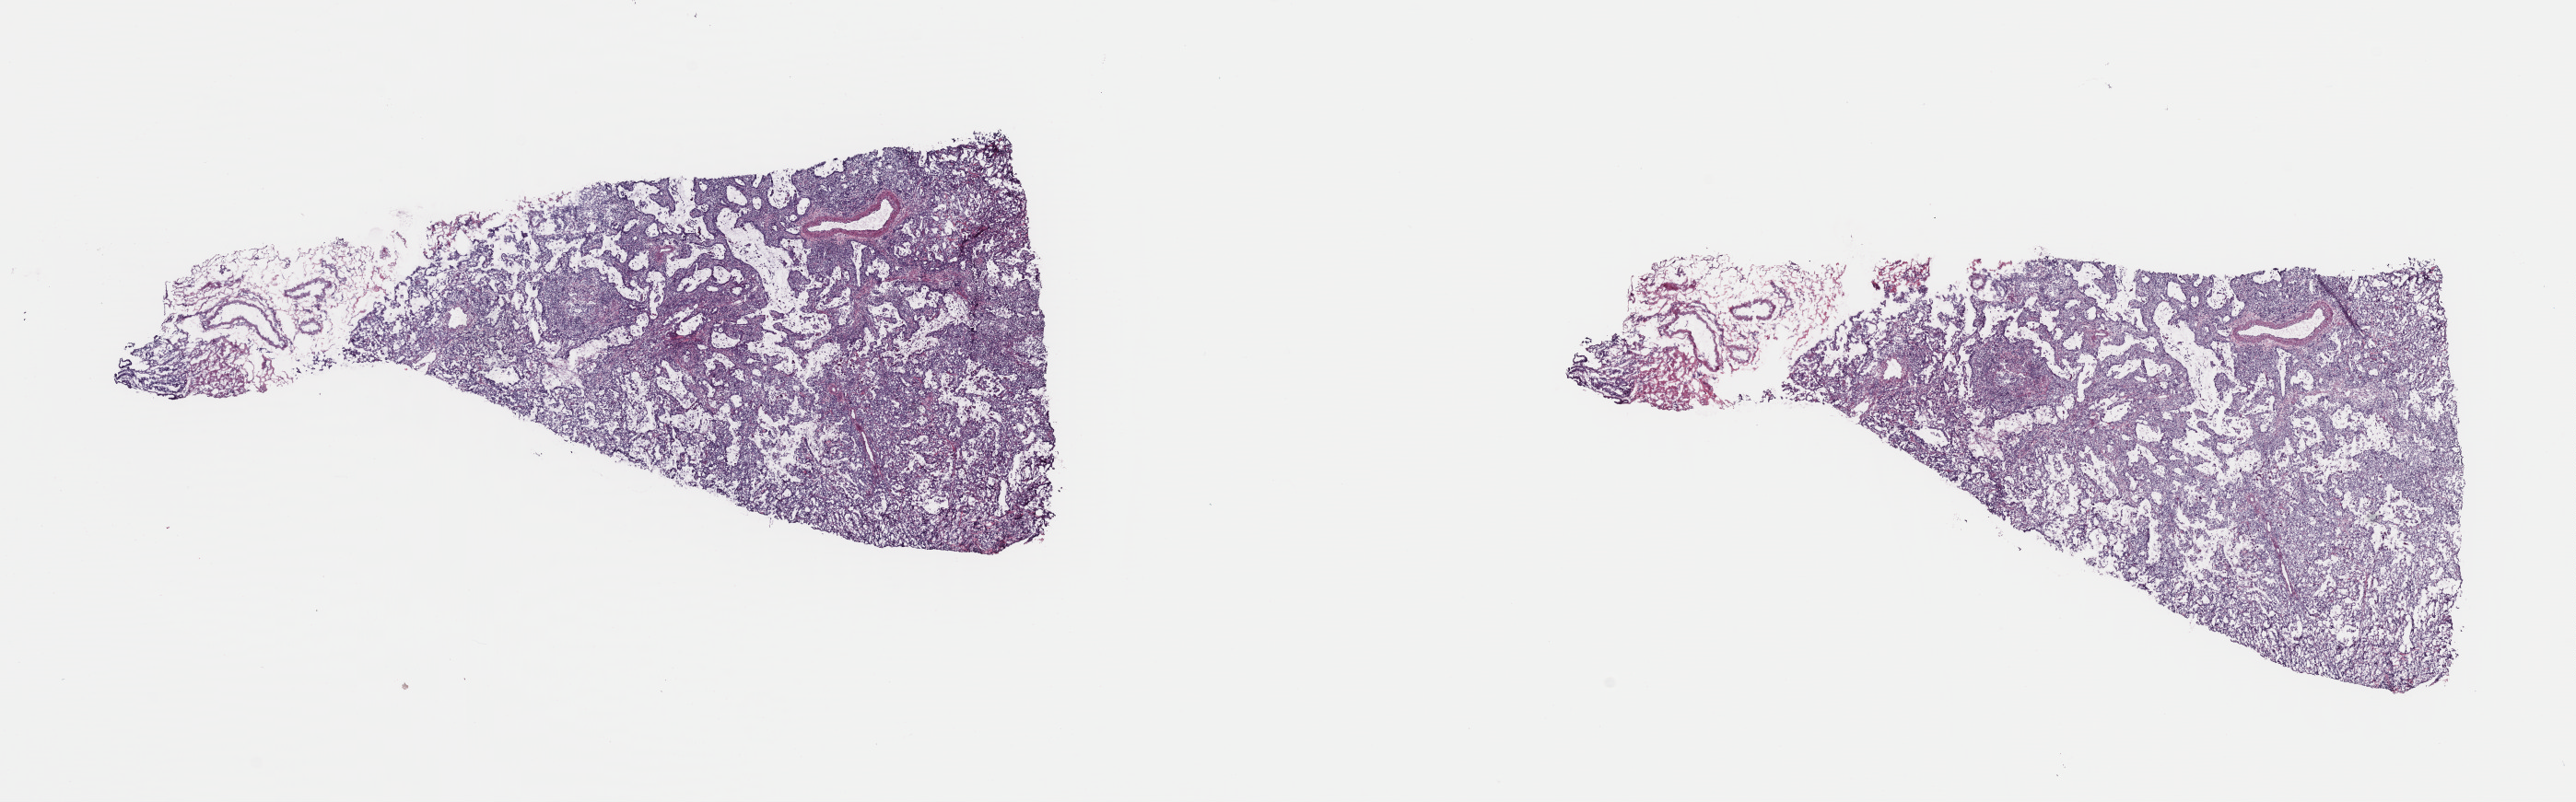
Digitized H&E-stained tissue section (whole slide) — whole scanned area (about 22.1 x 6.9 mm, from a 40x scan) shown as a low-resolution overview, frozen section from the top of the tissue portion, primary tumour sample from the esophagus. Patient: male, age at initial diagnosis 81 years. Histologic grade: GX (grade cannot be assessed). Composition of this section per pathologist review: tumour cells 100%, tumour nuclei 90%, normal cells 0%, stromal cells 0%, necrosis 0%. Inflammatory infiltration, as recorded: lymphocyte infiltration 0%, monocyte infiltration 0%, neutrophil infiltration 0%.
Diagnosis: Adenocarcinoma, NOS (lower third of esophagus). AJCC pathologic stage: IIA (6th edition). Lymph nodes positive (case pathology): 0 of 12 examined.